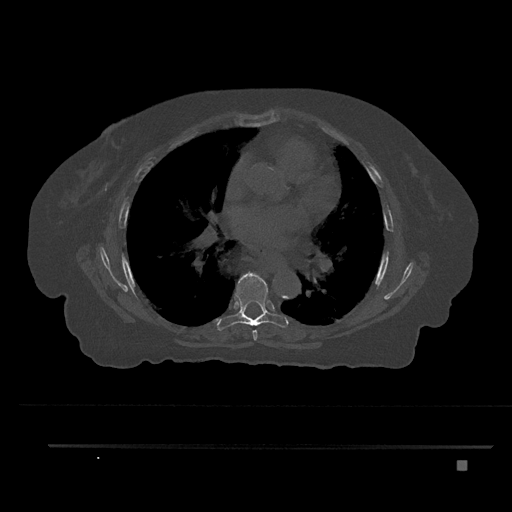
CT including the spine, one axial slice. Position 494 of 797 along the scan axis. Reconstruction kernel Br40s/3. 120 kVp. Bone window (W 1800 / L 400 HU). 0.5 mm slice thickness. 512 × 512 image matrix, field of view 437 × 437 mm. Female patient, age 76 years. Case-level facts recorded for this patient, not image findings: primary cancer: lung.
Annotated regions visible in this slice (semi-automatic segmentation, software-assisted and operator-edited):
- T6 vertebra: bounding box (x1, y1, x2, y2) in pixels: (252, 329, 258, 341)
- T7 vertebra: (217, 272, 289, 331)